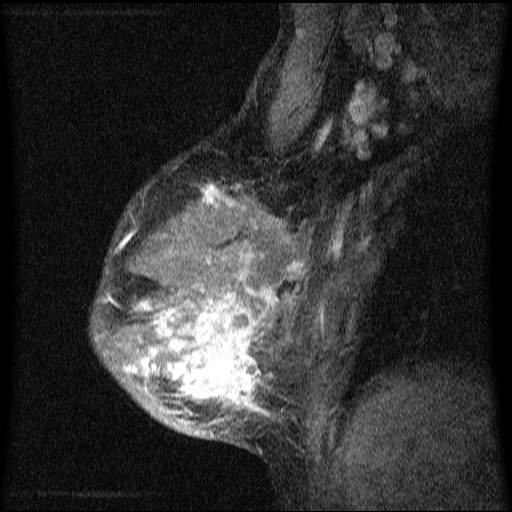
Breast MRI (dynamic contrast-enhanced), one sagittal slice. Position 48 of 64 along the scan axis. Dynamic contrast-enhanced series, image 2 of 4 at this slice position (ordered by acquisition). 1.5 T. TE 4.2 ms, TR 9.1 ms. 2 mm slice thickness. 512 × 512 image matrix, field of view 180 × 180 mm. Patient: female, 33 years.
Structures marked on this image (semi-automatically segmented with operator editing):
- analysis volume of interest (the breast-tissue region the enhancement analysis was run in; not a lesion): bounding box <90,153,334,451> (left, top, right, bottom; pixels)
- tumour enhancement mask (voxels above the 70 % enhancement threshold inside the analysis volume of interest): <105,184,301,420>